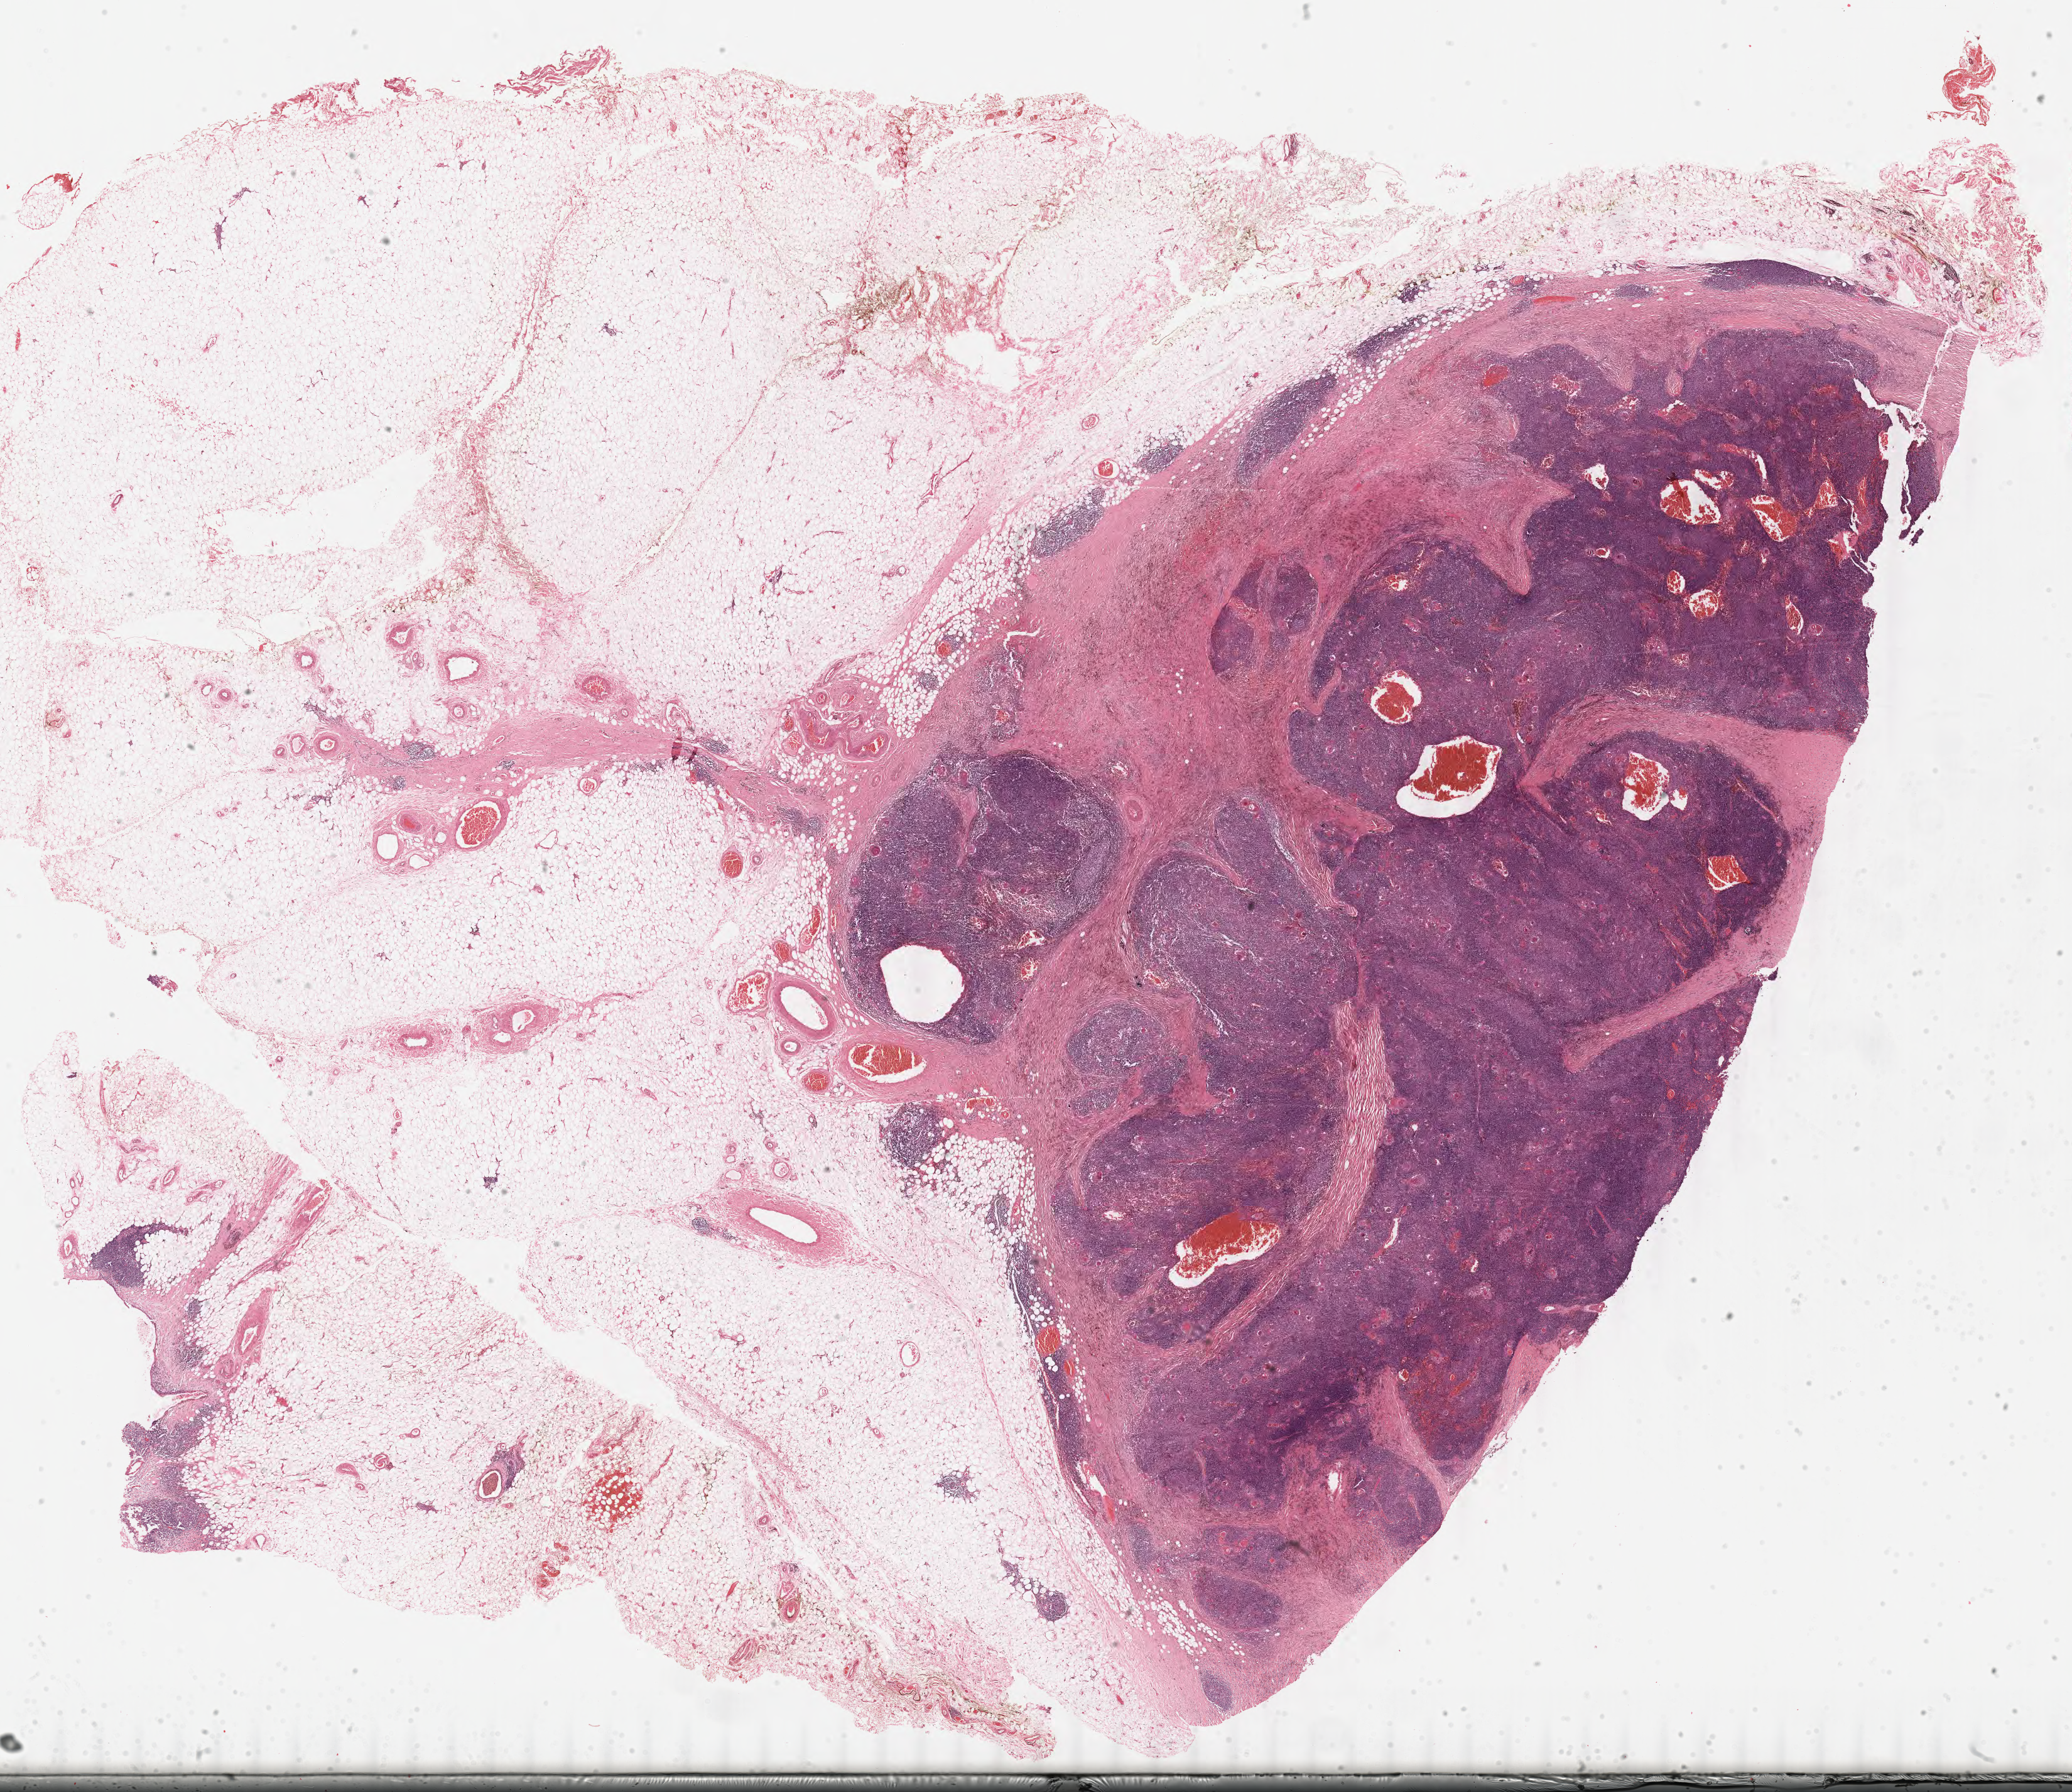
Whole-slide histology image, Hematoxylin and eosin (H&E) stained — whole scanned area (about 26.1 x 22.5 mm) shown as a low-resolution overview, formalin-fixed paraffin-embedded (FFPE) diagnostic section, primary tumour sample from the thymus. Male patient; age at initial diagnosis 63 years.
Diagnosis: Thymoma, type B3, malignant.